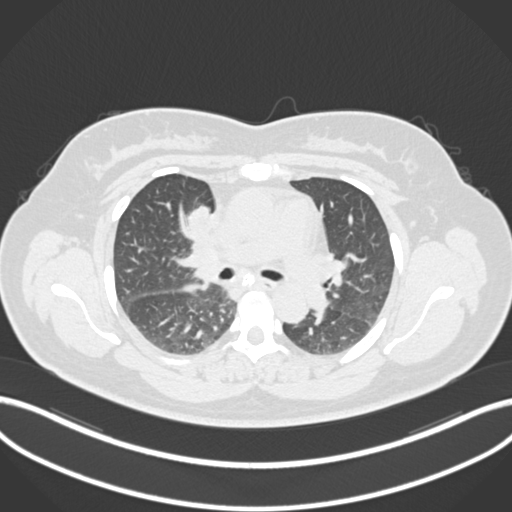
Chest CT, one axial slice; position 108 of 183 along the scan axis; reconstruction kernel B30f; 120 kVp; lung window (W 1500 / L -600 HU); 1 mm slice thickness; 512 × 512 image matrix. Patient: female, 46 years. From the clinical record (not read from this slice): clinical TNM (as recorded): T2a N1 M0.
Annotated regions visible in this slice (bounding box drawn by a radiologist):
- lung tumour (recorded histology: adenocarcinoma): bounding box <182,200,211,233> (left, top, right, bottom; pixels)